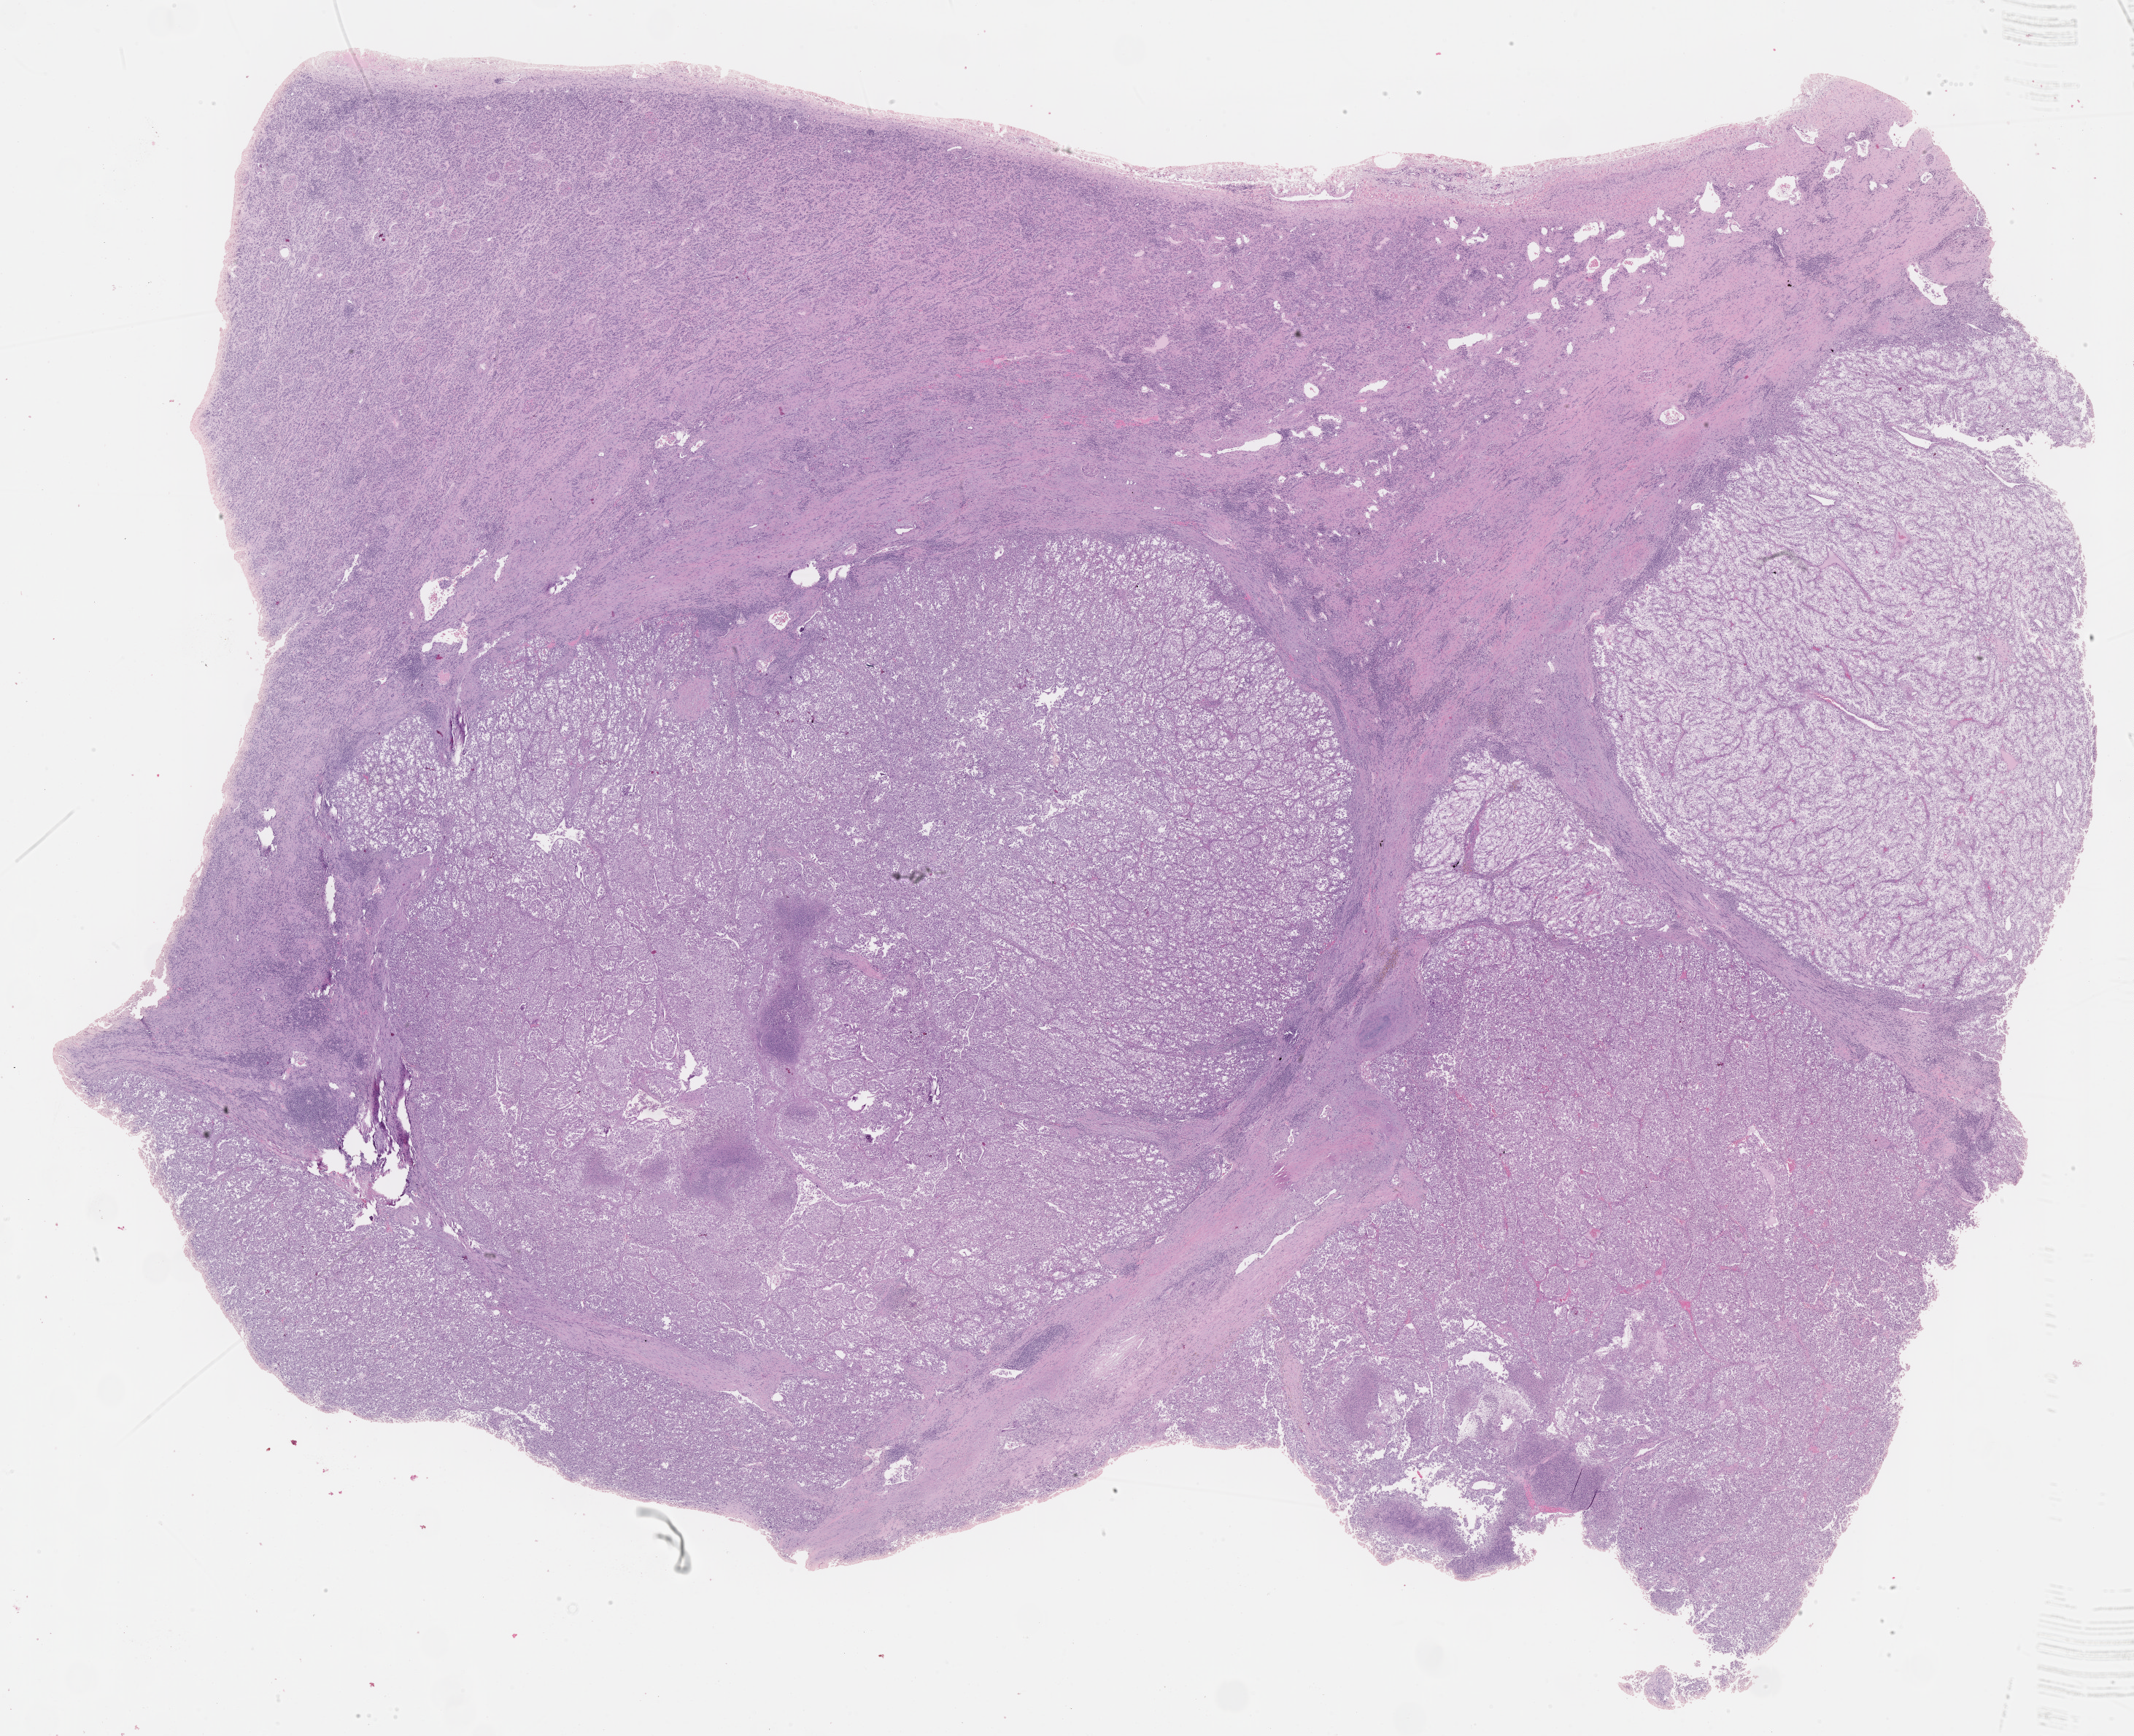
Hematoxylin and eosin (H&E) stained whole-slide image — shown as a low-resolution overview of the whole scanned area (about 23.6 x 19.2 mm). Formalin-fixed paraffin-embedded (FFPE) diagnostic section. Sample: primary tumour, kidney. Patient: male, age at initial diagnosis 41 years. Histologic grade: G3 (poorly differentiated).
AJCC pathologic stage: III. Histologic diagnosis: Clear cell adenocarcinoma, NOS.